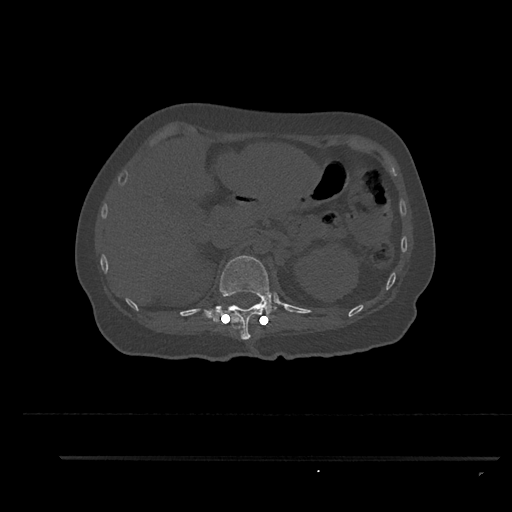
CT including the spine, one axial slice; slice 254 of 797 in the series (ordered by position); 120 kVp; bone window (W 1800 / L 400 HU); 0.5 mm slice thickness; 512 × 512 image matrix, field of view 408 × 408 mm. Female patient, age 44 years. Case-level facts recorded for this patient, not image findings: primary cancer: renal; vertebrae with lytic lesions (as recorded): L1.
Annotated regions visible in this slice (semi-automatic segmentation, software-assisted and operator-edited):
- T12 vertebra: bounding box <203,255,277,340> (left, top, right, bottom; pixels)